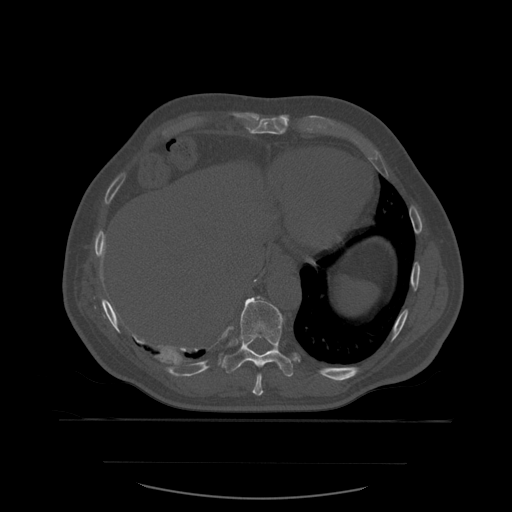
CT including the spine, one axial slice. Slice 321 of 590 in the series (ordered by position). Bone window (W 1800 / L 400 HU). 1.25 mm slice thickness. 512 × 512 image matrix, field of view 479 × 479 mm. Patient age 71 years. Case-level facts recorded for this patient, not image findings: primary cancer: lung; vertebrae with lytic lesions (as recorded): T1, T2, L5, S1.
Annotated regions visible in this slice (semi-automatically segmented with operator editing):
- T10 vertebra: box from (x=225, y=296) to (x=297, y=377) px
- T9 vertebra: (x=253, y=374)–(x=264, y=396)